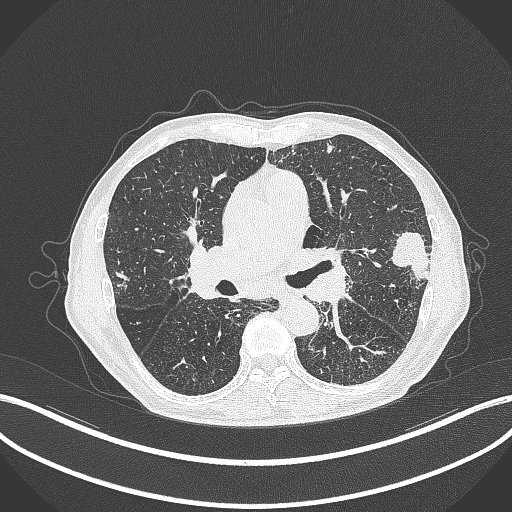
Chest CT, one axial slice. Position 233 of 463 along the scan axis. Reconstruction kernel B70f. 120 kVp. Lung window (W 1500 / L -600 HU). 512 × 512 image matrix, field of view 400 × 400 mm. Male patient, age 74 years. Case-level facts recorded for this patient, not image findings: clinical TNM (as recorded): T2a N1 M0.
Annotated regions visible in this slice (bounding box drawn by a radiologist):
- lung tumour (recorded histology: adenocarcinoma): bounding box [x1, y1, x2, y2] px = [385, 226, 431, 287]